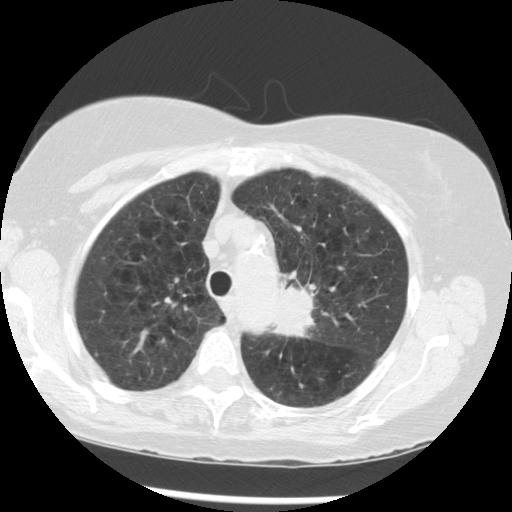
Chest CT (low-dose screening protocol), one axial image. Third screening round (two years after baseline). Lung window (W 1500 / L -600 HU). 2.5 mm slice thickness. Standard (soft-tissue) reconstruction kernel (STANDARD). Slice 217 of 283 in the series. Female, age 70 years at enrolment. Current smoker at enrolment.
Expert-annotated lung lesion, bounding box (x1, y1, x2, y2) in pixels: (264, 269, 358, 359). Screening reader's record for this exam (one nodule recorded; not confirmed to be the boxed lesion): non-calcified nodule or mass ≥4 mm, left upper lobe, 32 × 26 mm, spiculated (stellate) margins, soft tissue attenuation, pre-existing on the prior screen: yes; interval growth: yes. Later outcome: lung cancer diagnosed 24 days after this screen — neoplasm, malignant, left upper lobe, stage IIIB (AJCC 6th edition), 40 mm at pathology.